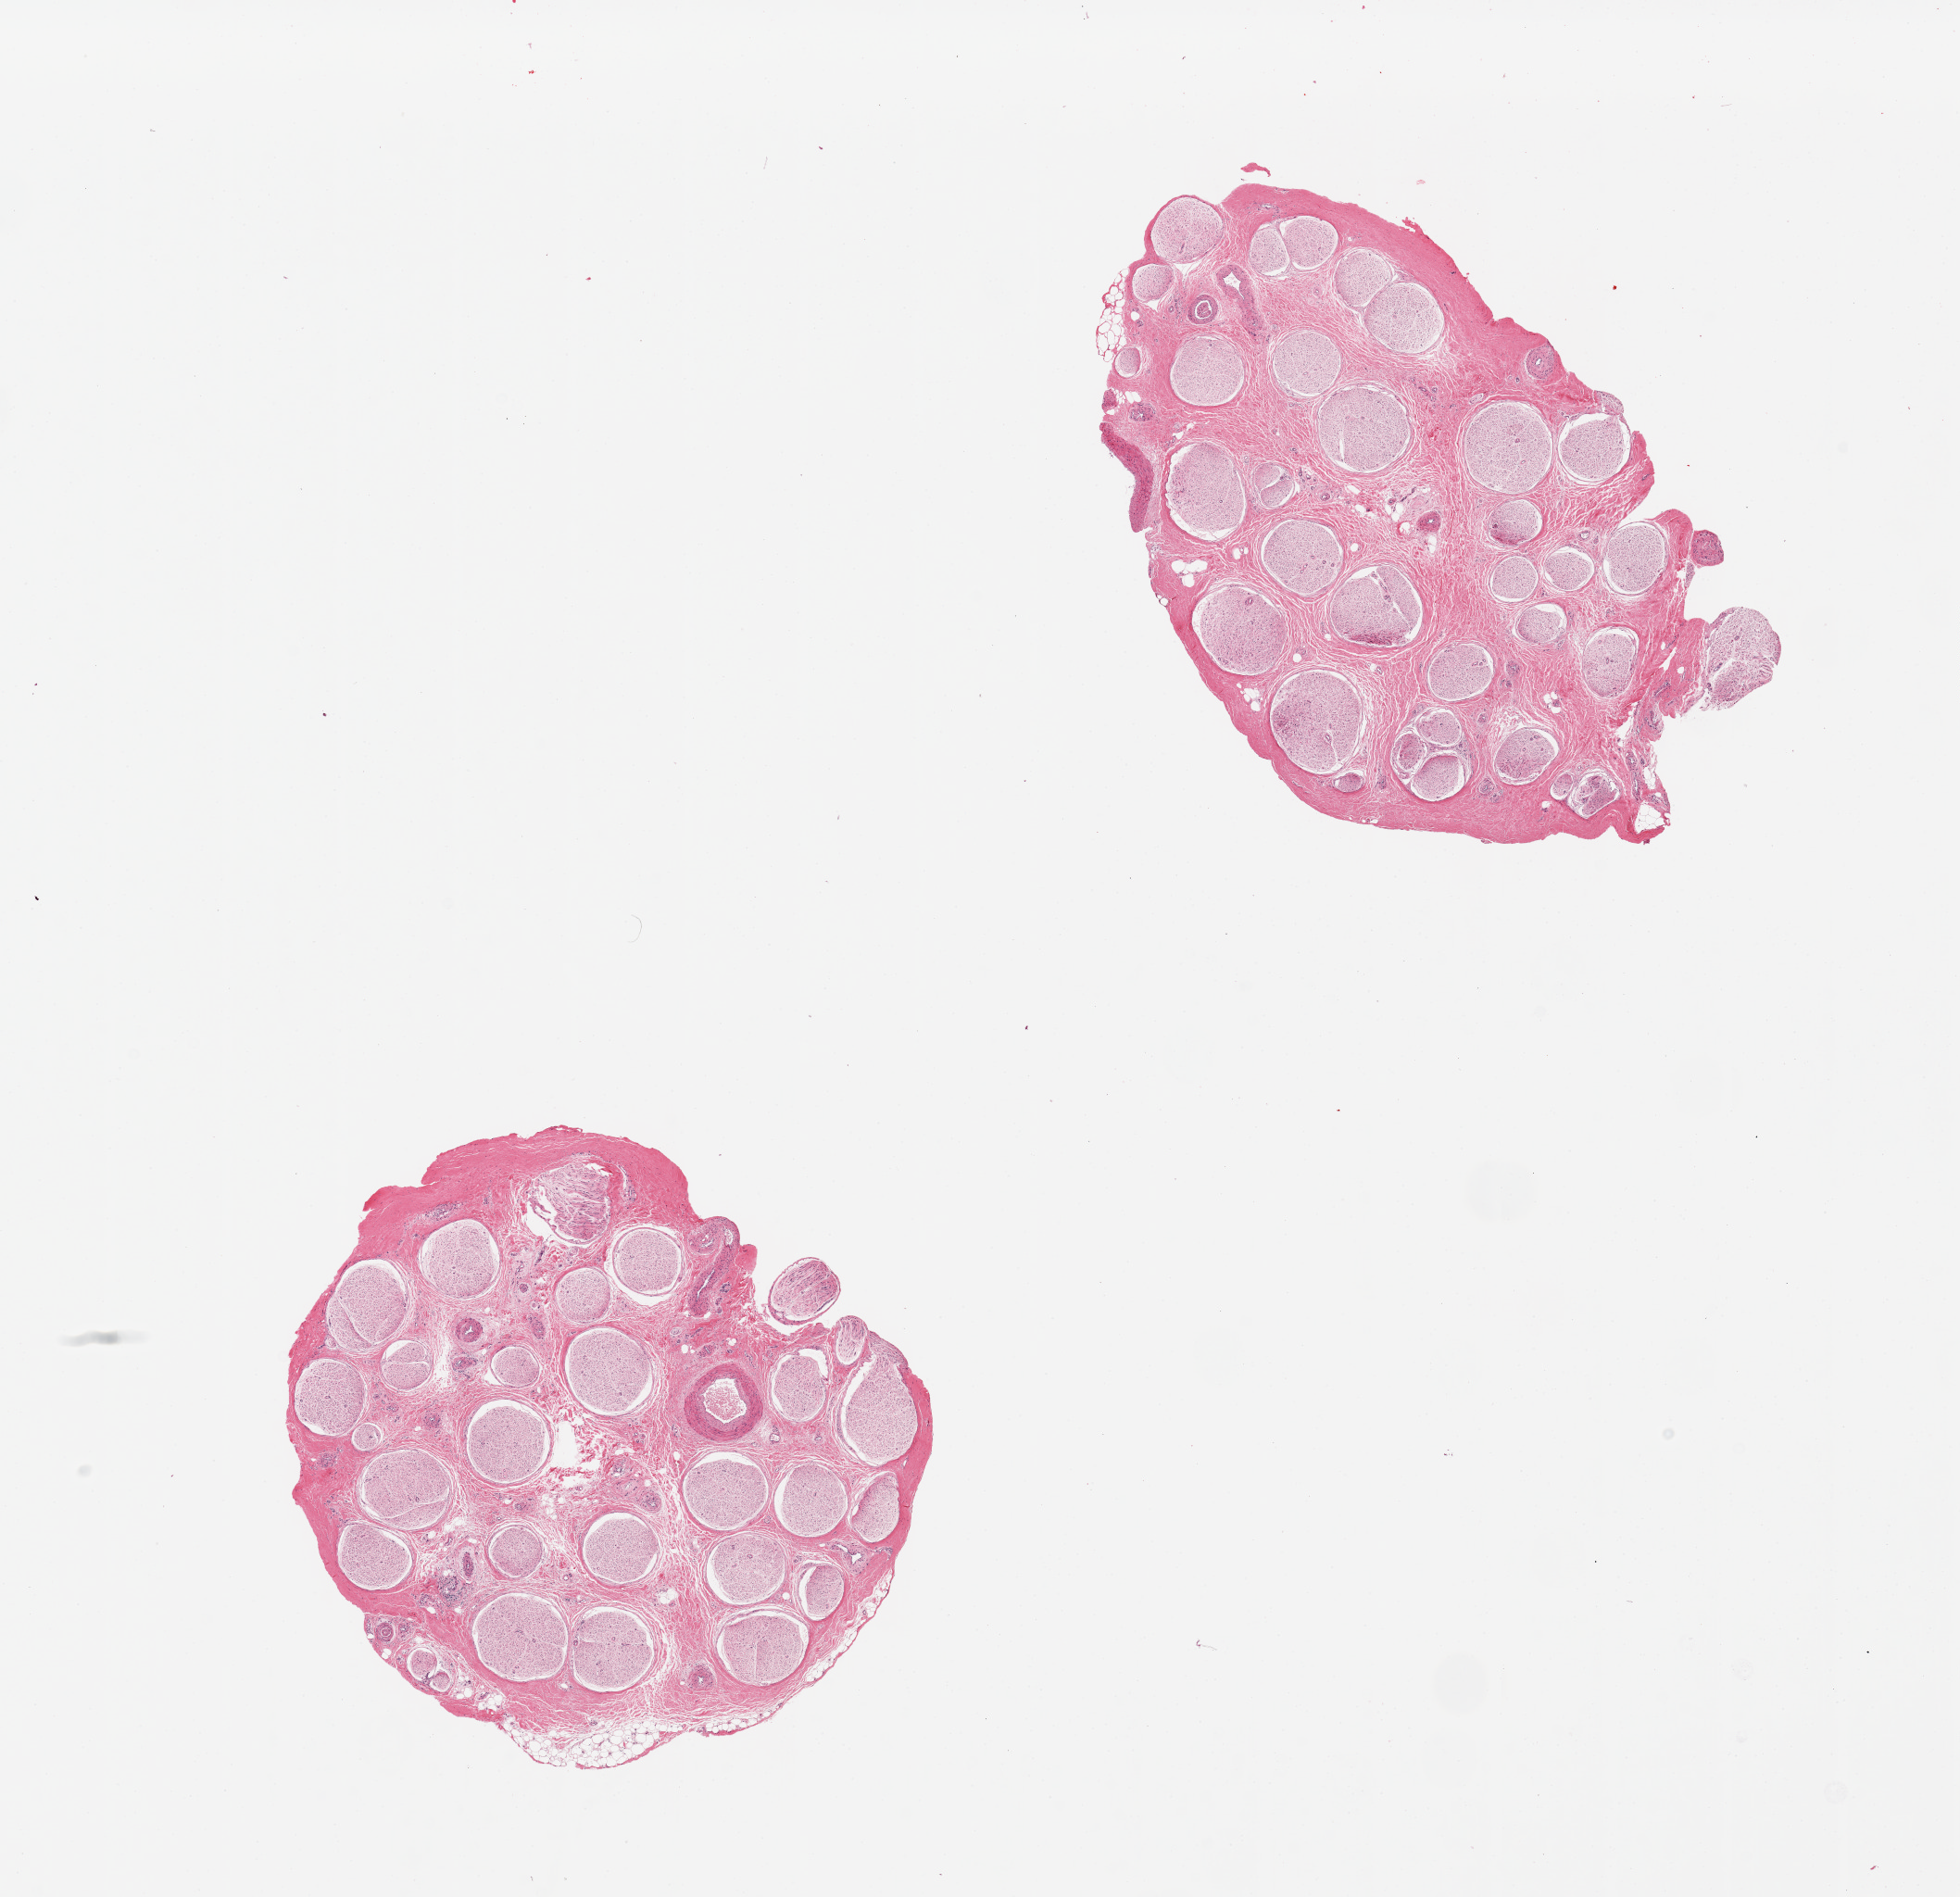
H&E whole-slide image, whole scanned area (about 16.7 x 16.2 mm, slide scanned at 20x) shown as a low-resolution overview, PAXgene-fixed, paraffin-embedded tissue, target tissue: tibial nerve, donor tissue sample. Donor: male.
Reviewer comment on this tissue sample: 2 pieces. Prominent (diabetic) small artery disease (thickening). Stromal fibrosis. Nerve fibers appear atrophic.